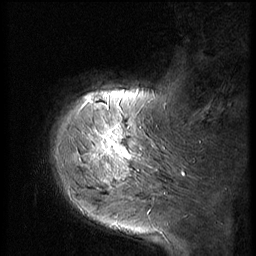
Breast MRI (dynamic contrast-enhanced), one sagittal slice. Slice 11 of 56 in the series (ordered by position). Dynamic contrast-enhanced series, image 2 of 2 at this slice position (ordered by acquisition). 1.5 T. TE 4.2 ms, TR 9 ms. 2.5 mm slice thickness. 256 × 256 image matrix, field of view 180 × 180 mm. Patient: female, 51 years. Case-level facts recorded for this patient, not image findings: setting: breast cancer imaged before/during neoadjuvant chemotherapy; receptor status: triple-negative.
Annotated regions visible in this slice (semi-automatic segmentation, software-assisted and operator-edited):
- analysis volume of interest (the breast-tissue region the enhancement analysis was run in; not a lesion): bounding box (x1, y1, x2, y2) in pixels: (60, 98, 147, 197)
- tumour enhancement mask (voxels above the 140 % enhancement threshold inside the analysis volume of interest): (90, 98, 129, 183)